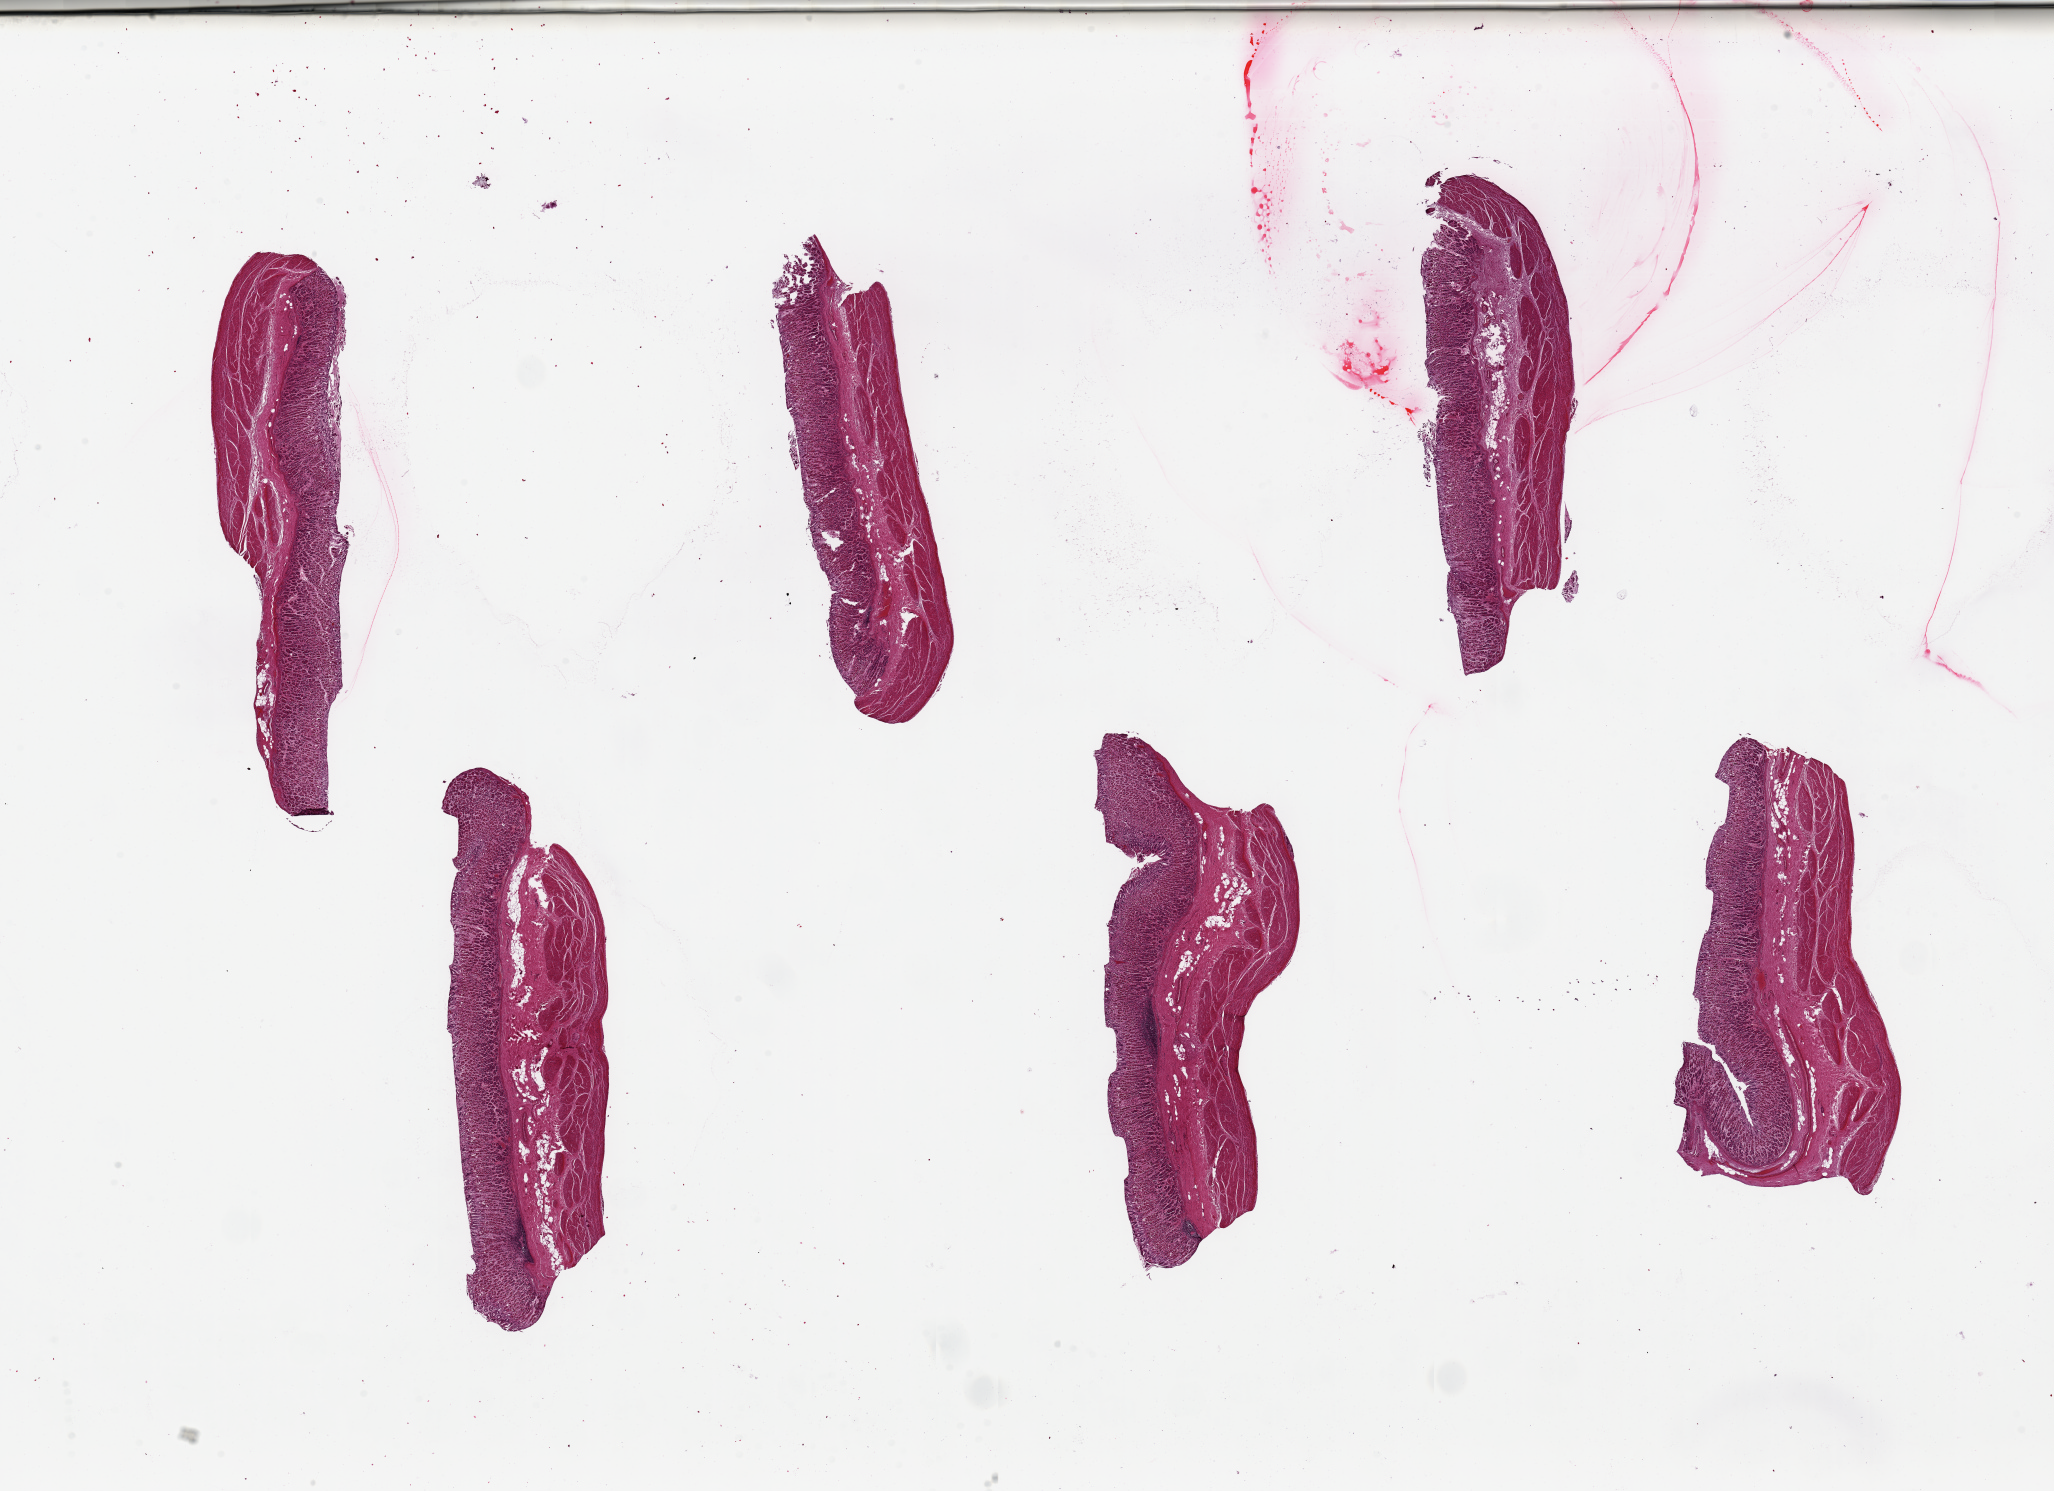
Whole-slide image, haematoxylin and eosin stain, brightfield — shown as a low-resolution overview of the whole scanned area (about 32.5 x 23.6 mm), PAXgene-fixed paraffin-embedded (PFPE) section, target tissue: stomach, donor tissue sample.
Pathologist's review note for this sample: 6 pieces, up to 9x2mm; mucosa prservation ranges from score 1 to score 2 ~30--40% thickness.